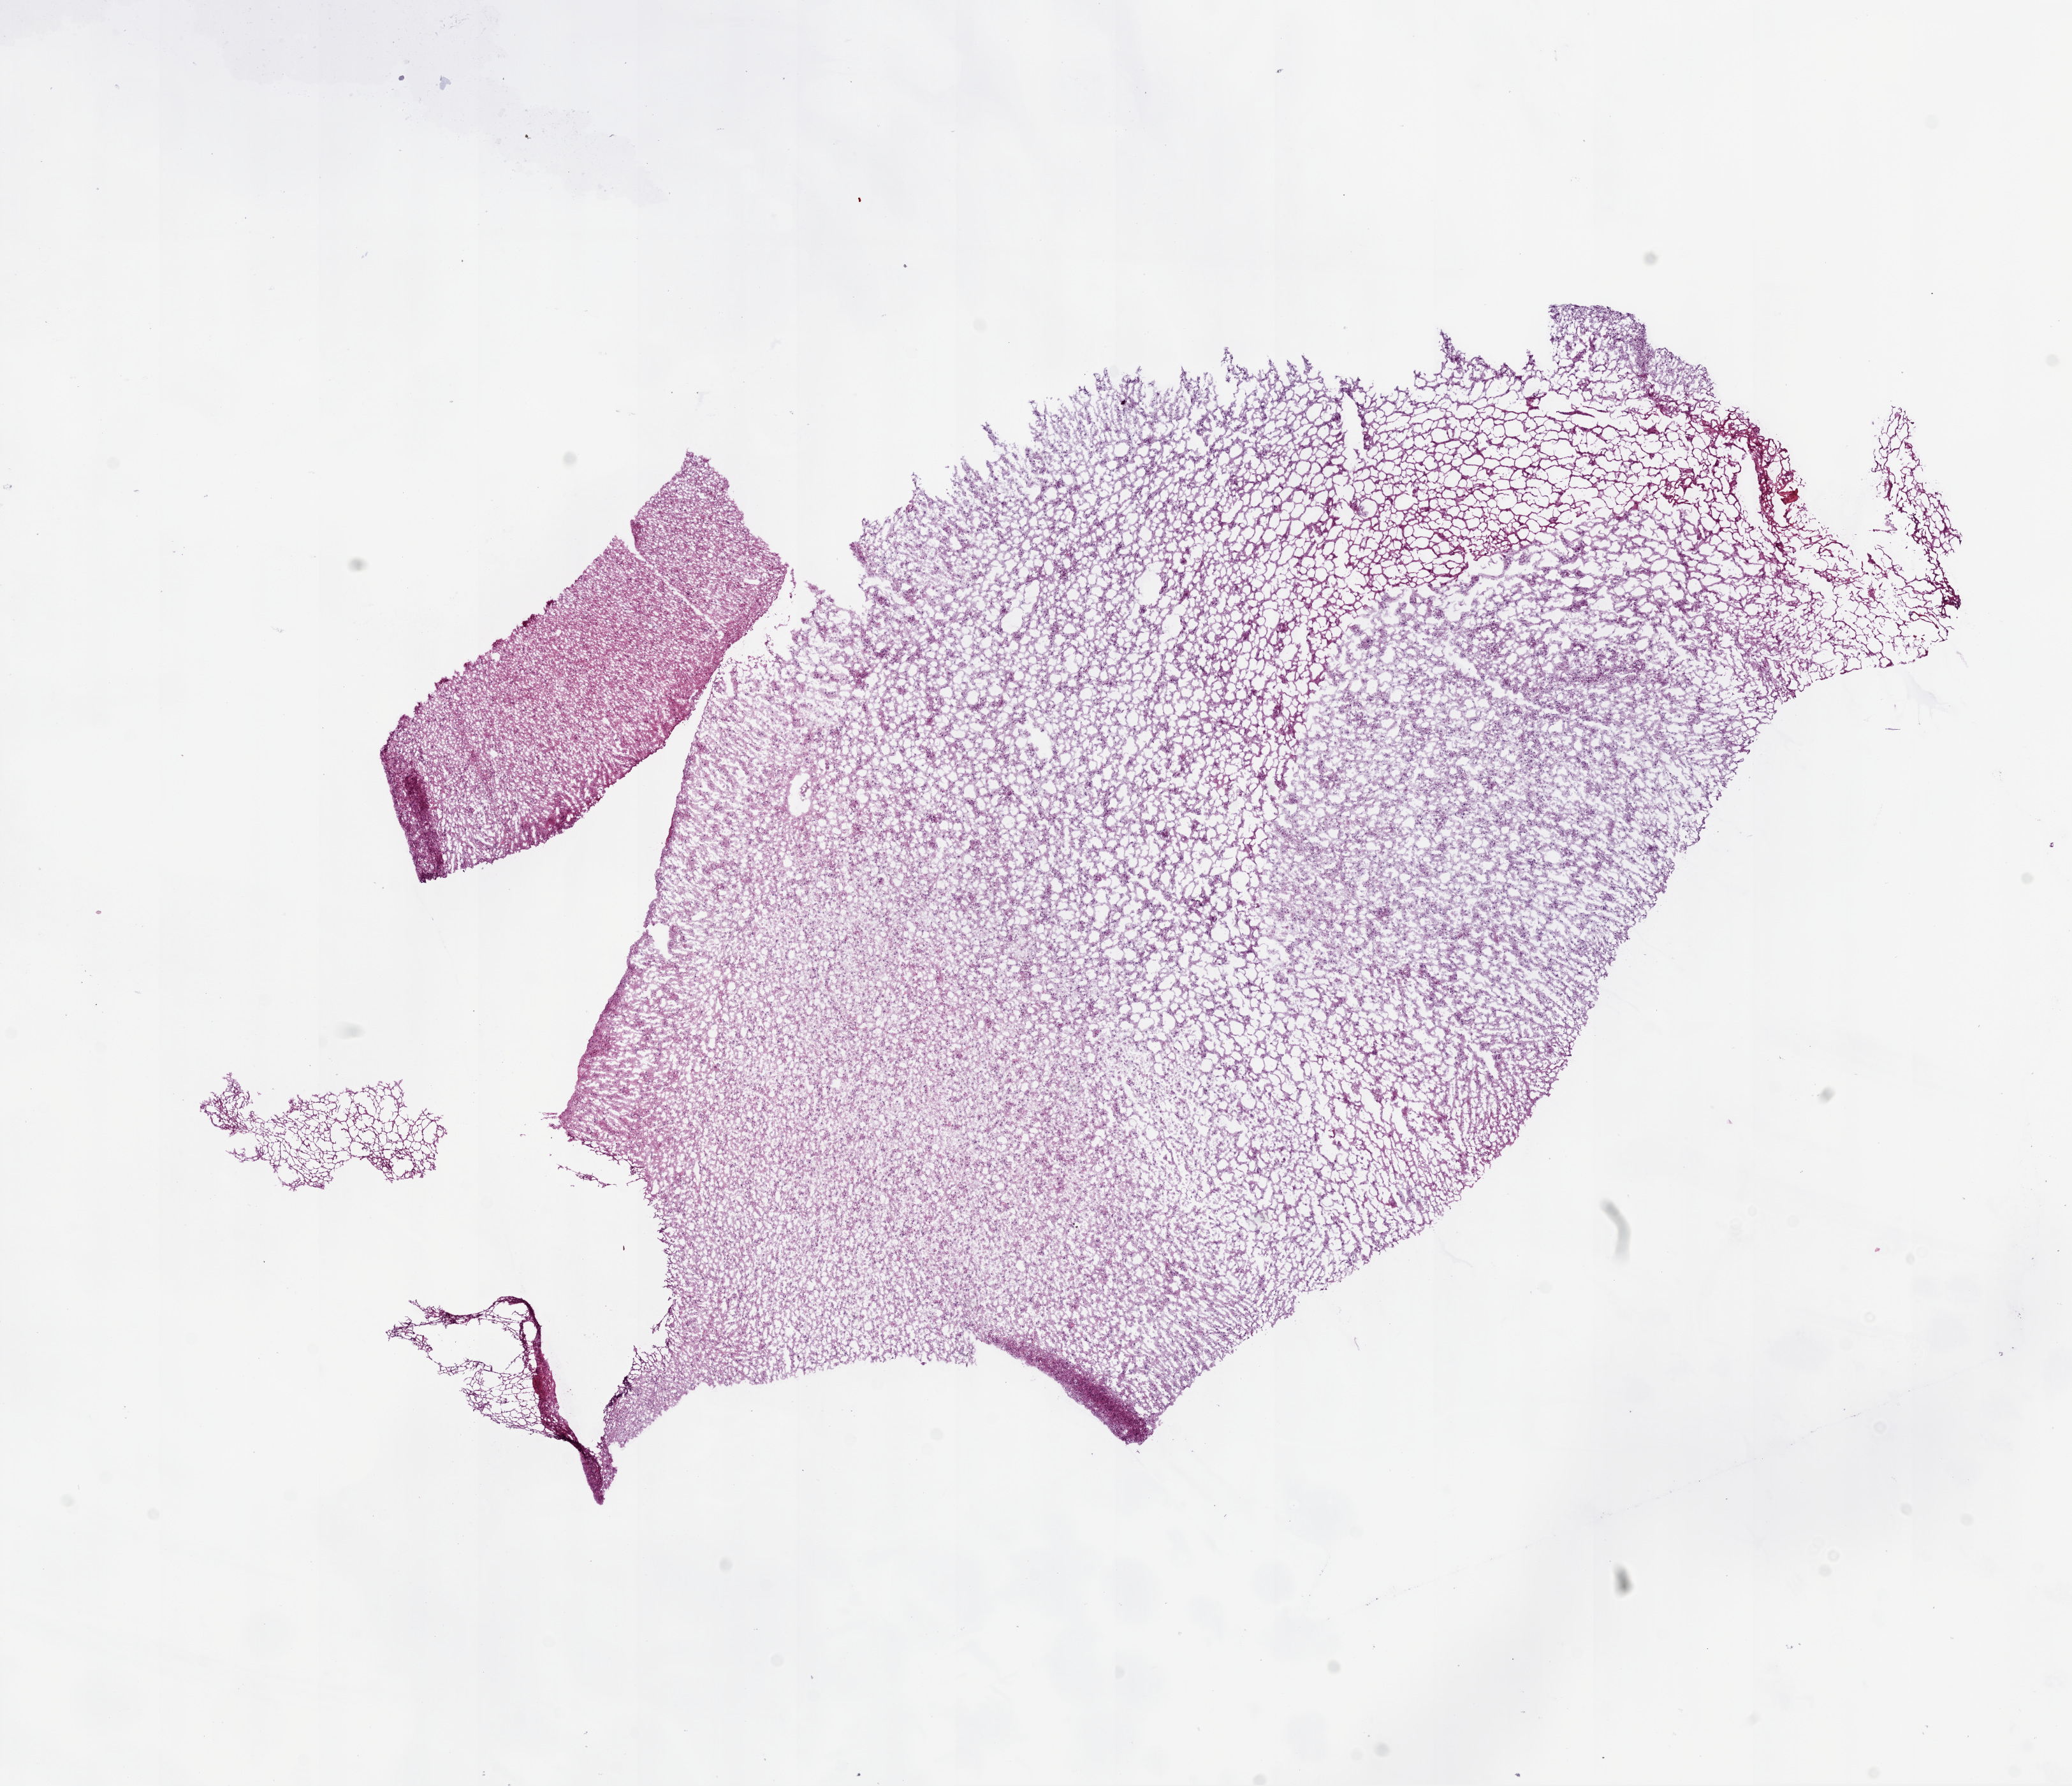
Whole-slide histology image, H&E — shown as a low-resolution overview of the whole scanned area (about 13.0 x 11.2 mm, slide scanned at 20x); frozen section; sample: primary tumour, brain. Patient: male, age at initial diagnosis 38 years. Histologic grade: G3 (poorly differentiated). Slide review estimates, as recorded: tumour cells 100%, tumour nuclei 70%, normal cells 0%, stromal cells 0%, necrosis 0%.
Laterality: left. Histologic diagnosis: Astrocytoma, anaplastic.